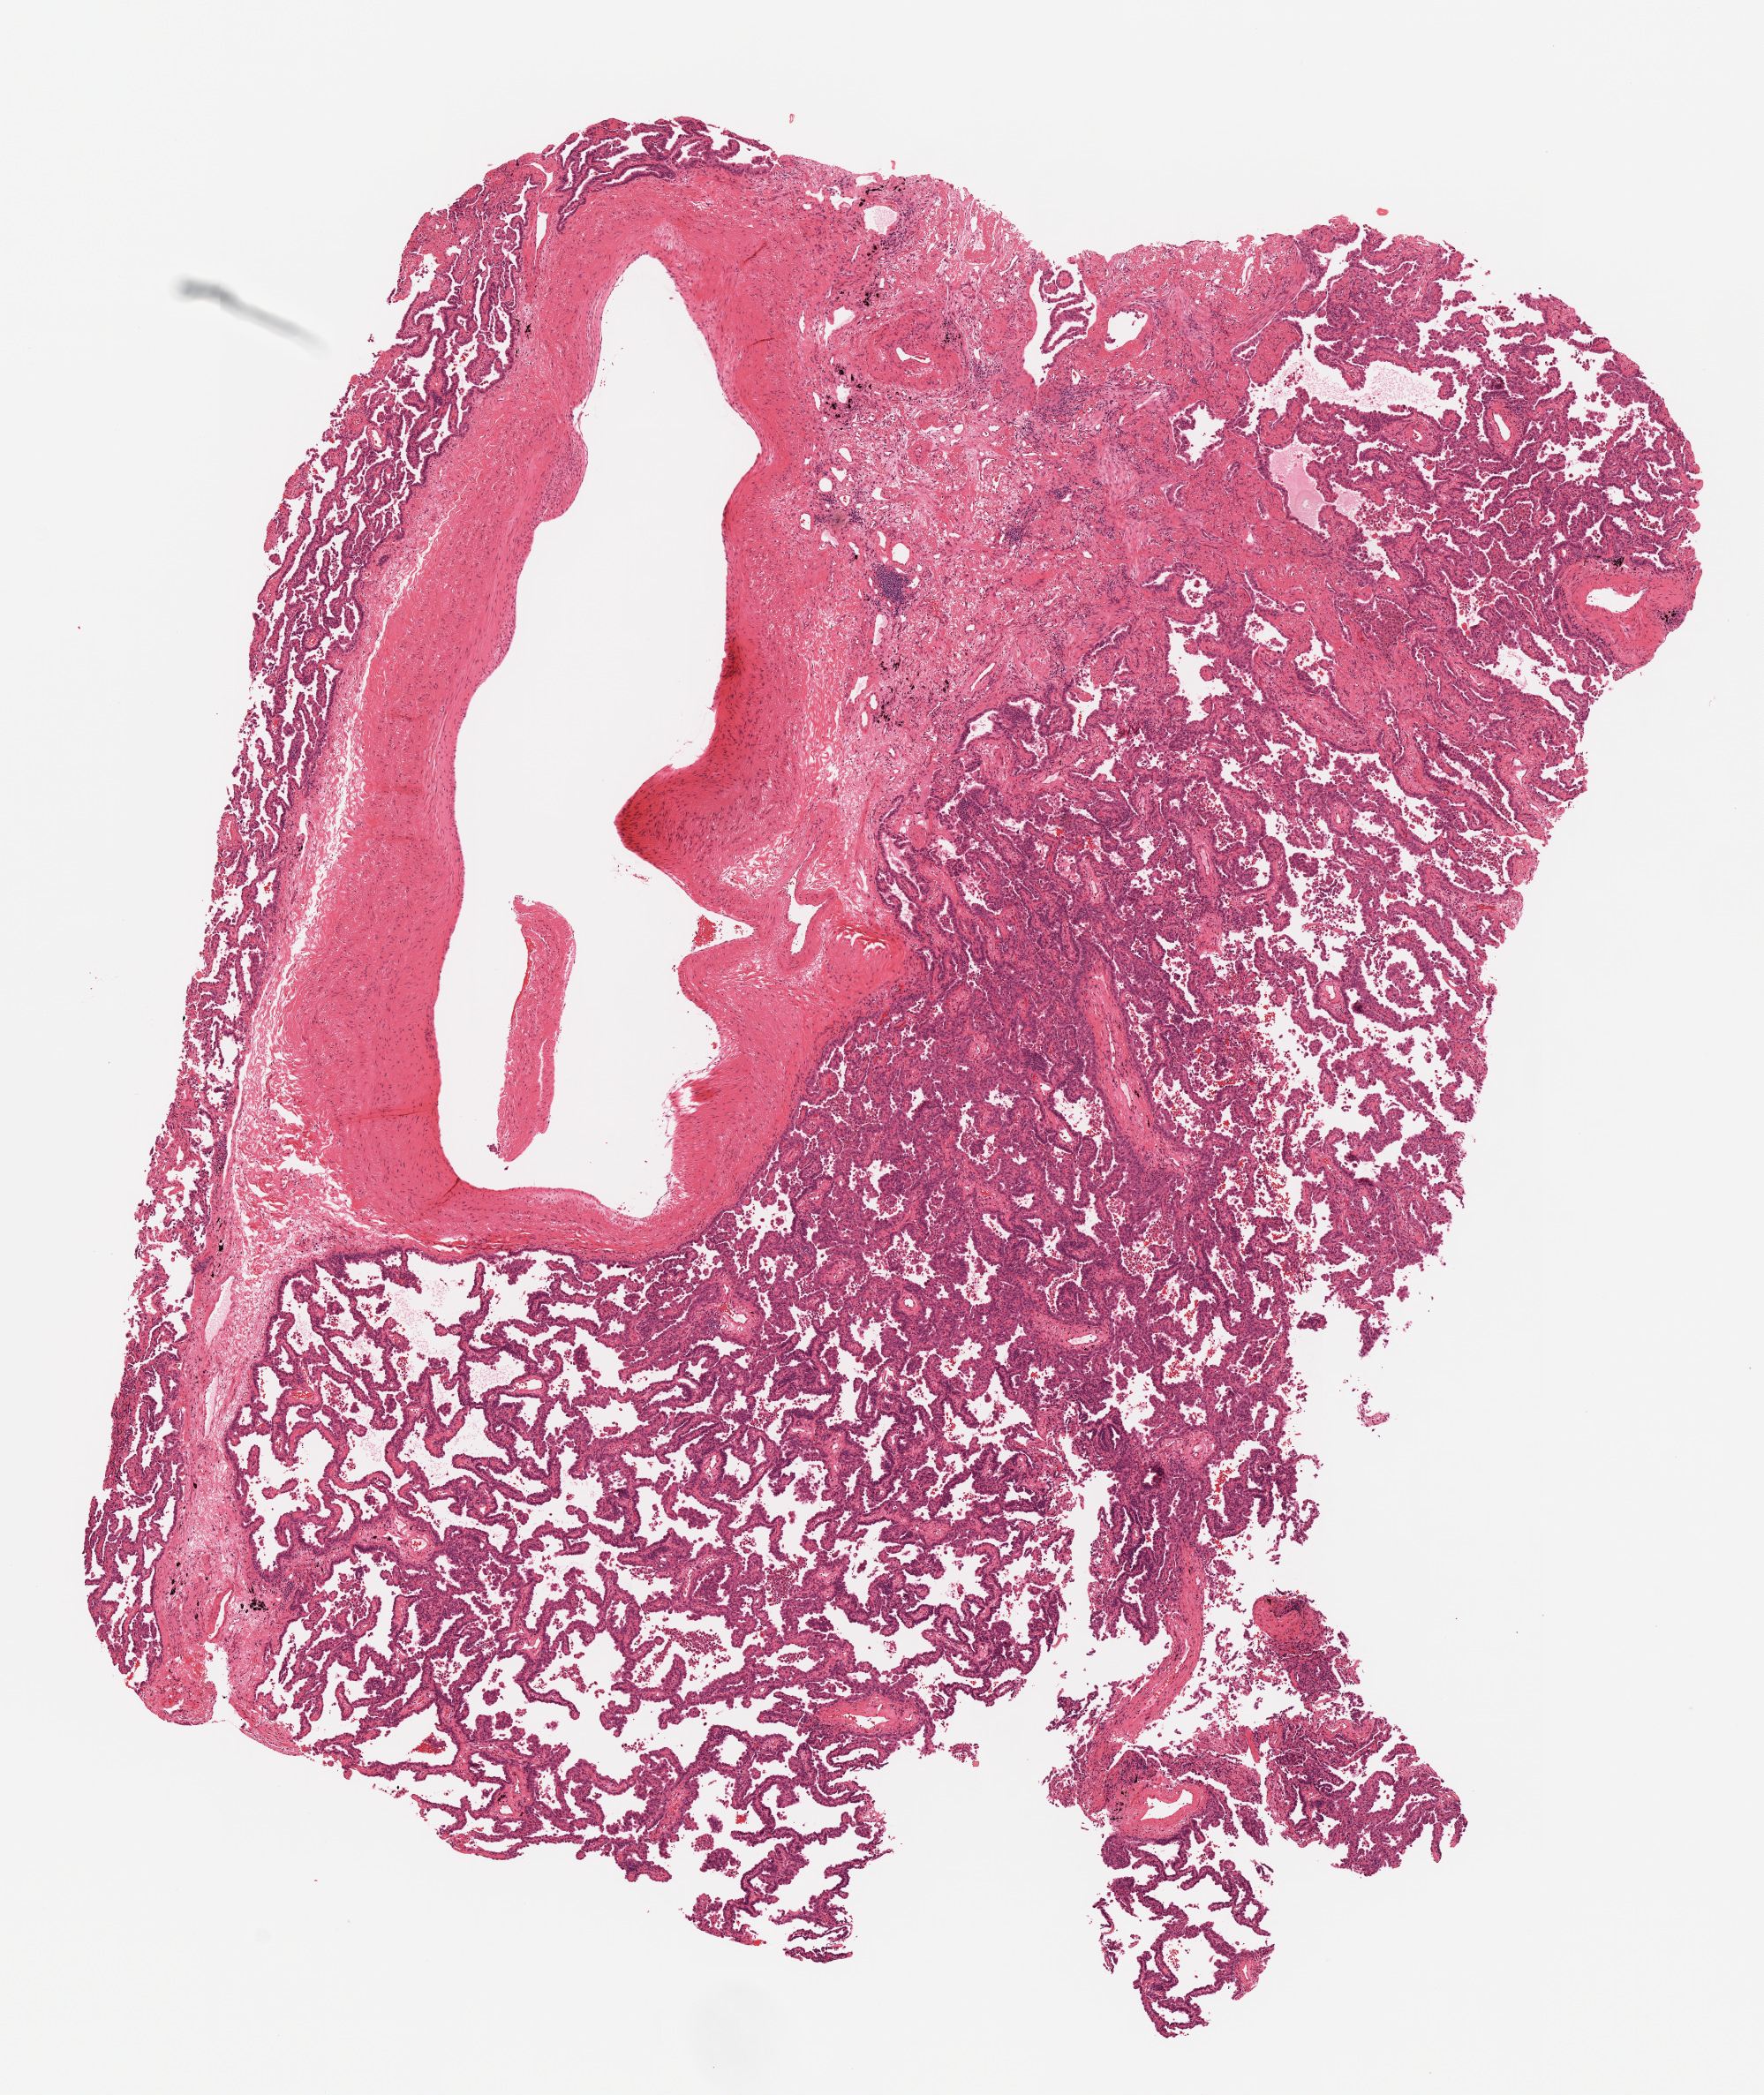
Whole-slide histology image, Hematoxylin and eosin (H&E) stained — shown as a low-resolution overview of the whole scanned area (about 8.0 x 9.5 mm). Formalin-fixed paraffin-embedded (FFPE) diagnostic section. Sample: primary tumour, lung. Male patient.
* laterality: right
* pathologic diagnosis: Adenocarcinoma, NOS (upper lobe, lung)
* AJCC pathologic stage: IB